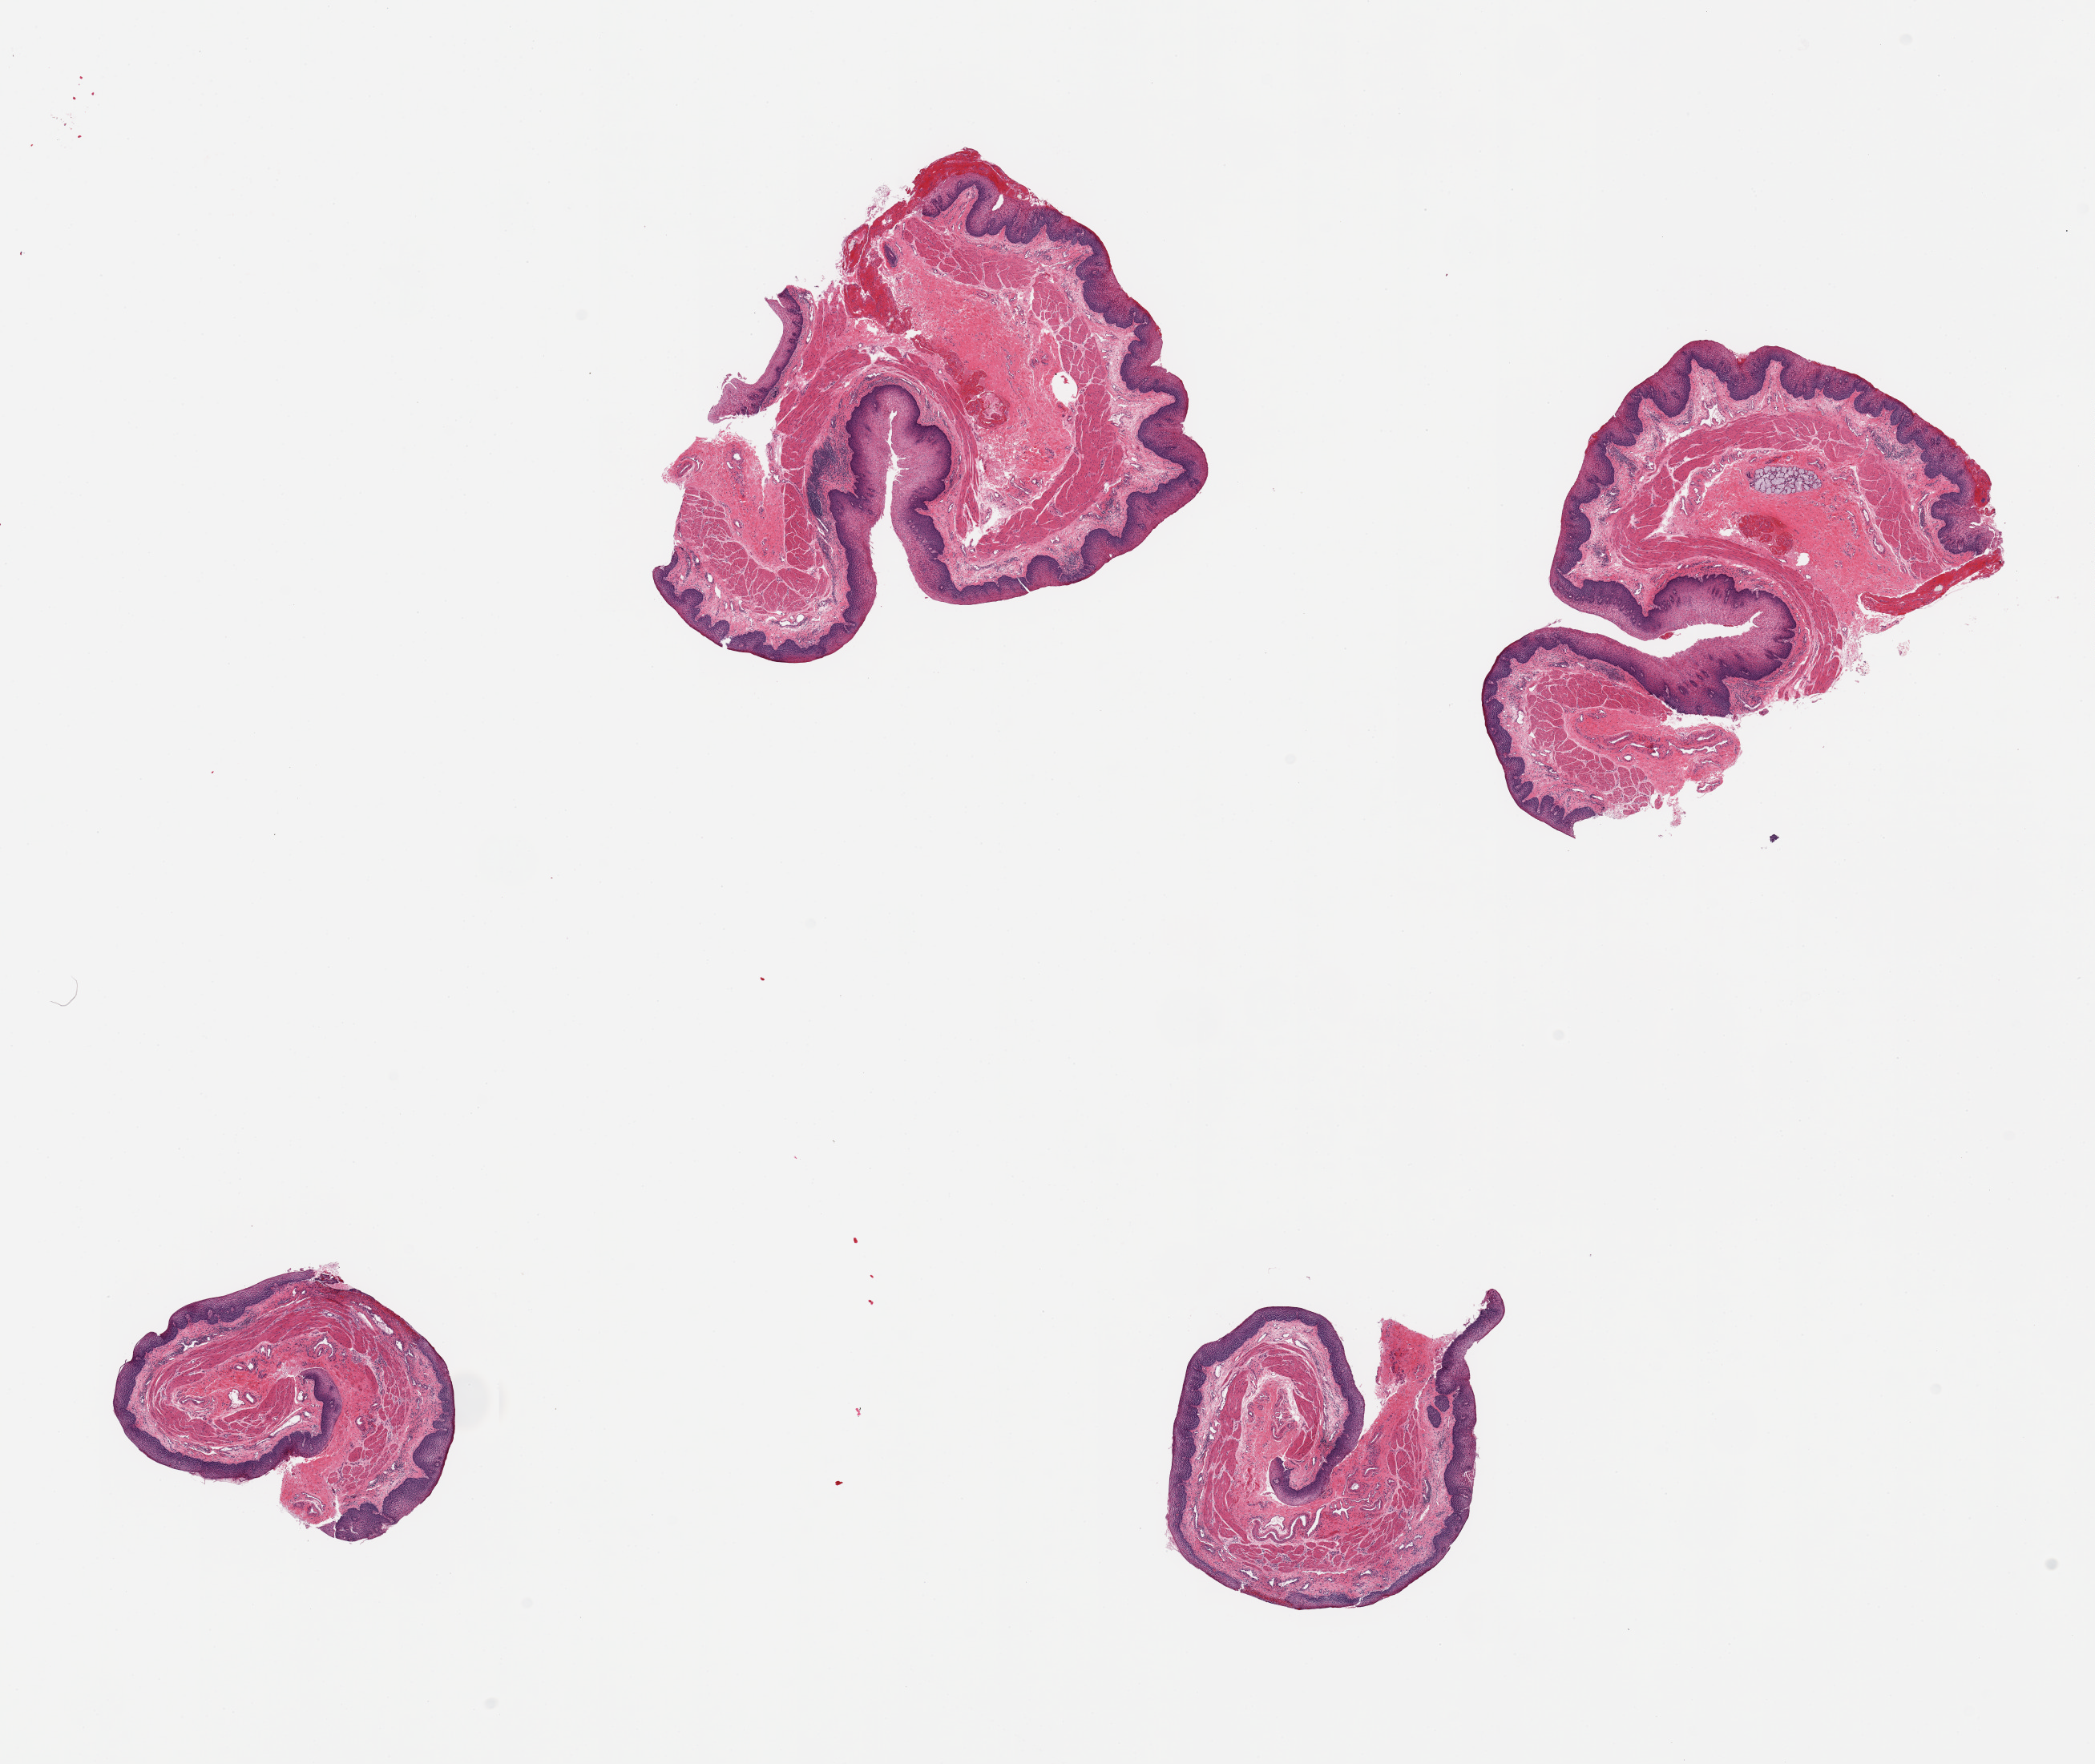
Digitized hematoxylin and eosin (H&E)-stained section — whole scanned area (about 20.7 x 17.4 mm) shown as a low-resolution overview. PAXgene-fixed, paraffin-embedded tissue. Section of esophageal mucous membrane (target tissue). Tissue donor sample. Male donor.
Review note (as recorded): 4 pieces; 2 erosions; focal mild esophagitis.